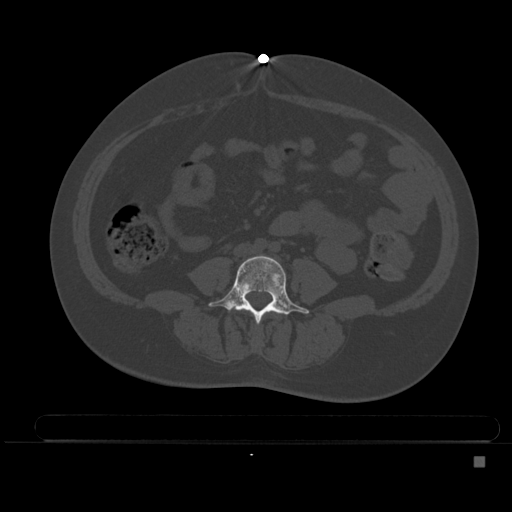
CT including the spine, one axial slice; bone window (W 1800 / L 400 HU); 1.5 mm slice thickness; 512 × 512 image matrix, field of view 404 × 404 mm. Female patient, age 33 years. Case-level facts recorded for this patient, not image findings: primary cancer: breast; vertebrae with lytic lesions (as recorded): T1.
Structures marked on this image (semi-automatic segmentation, software-assisted and operator-edited):
- L4 vertebra: bounding box <208,255,309,323> (left, top, right, bottom; pixels)